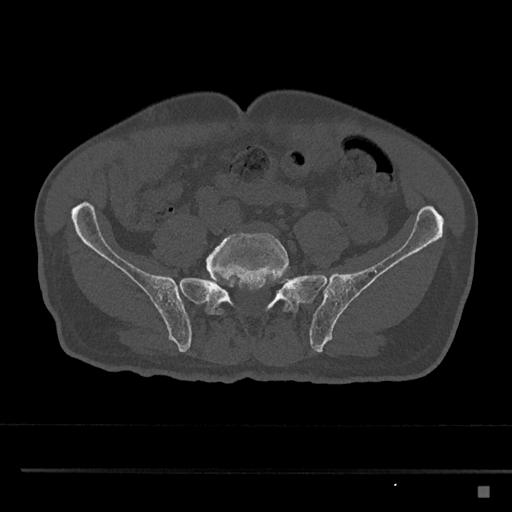
CT including the spine, one axial slice. Slice 557 of 797 in the series (ordered by position). Reconstruction kernel Br40s/3. 120 kVp. Bone window (W 1800 / L 400 HU). 512 × 512 image matrix, field of view 391 × 391 mm. Male patient, age 59 years. From the clinical record (not read from this slice): primary cancer: prostate.
Annotated regions visible in this slice (semi-automatically segmented with operator editing):
- L5 vertebra: box from (x=206, y=232) to (x=291, y=315) px